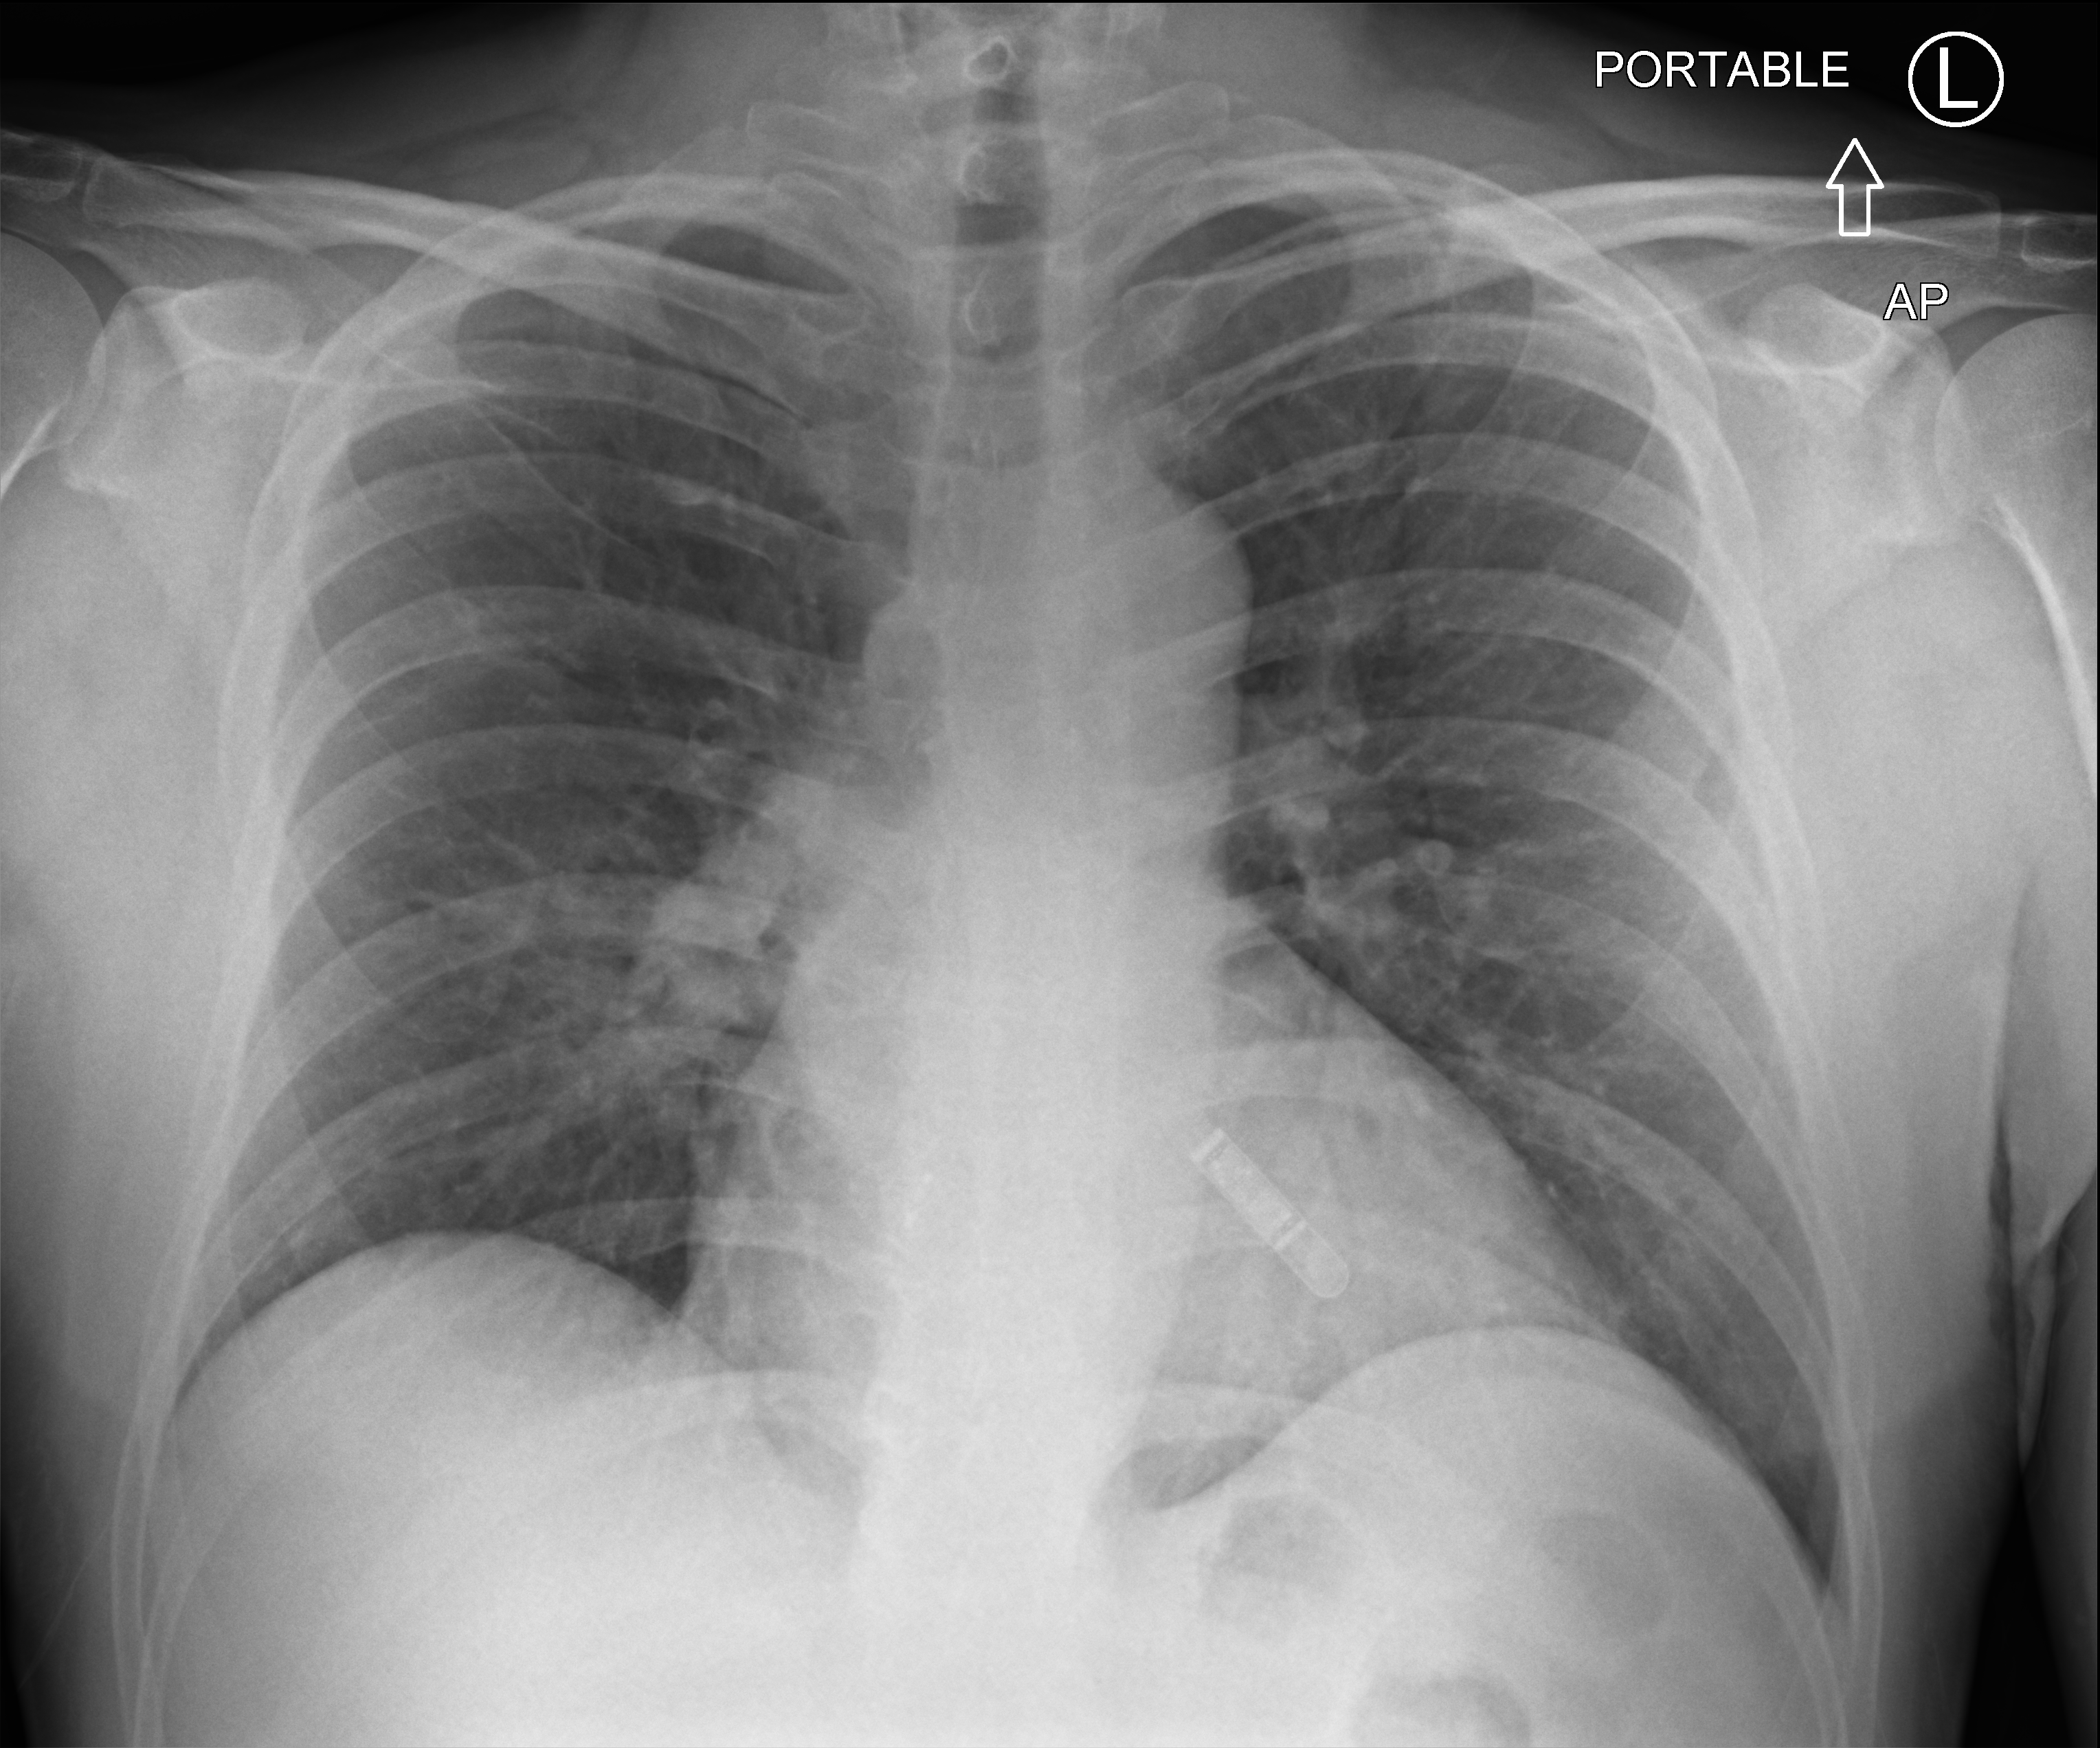
Chest X-ray (portable), anteroposterior (AP) projection. Patient hospitalised with COVID-19; male, aged 18–59 years.
From the hospital-stay record, not from the radiograph (when in the stay this image was taken is not recorded): admitted to intensive care during this hospital stay: no; other chronic lung disease (admission record): no; chronic kidney disease (admission record): no.